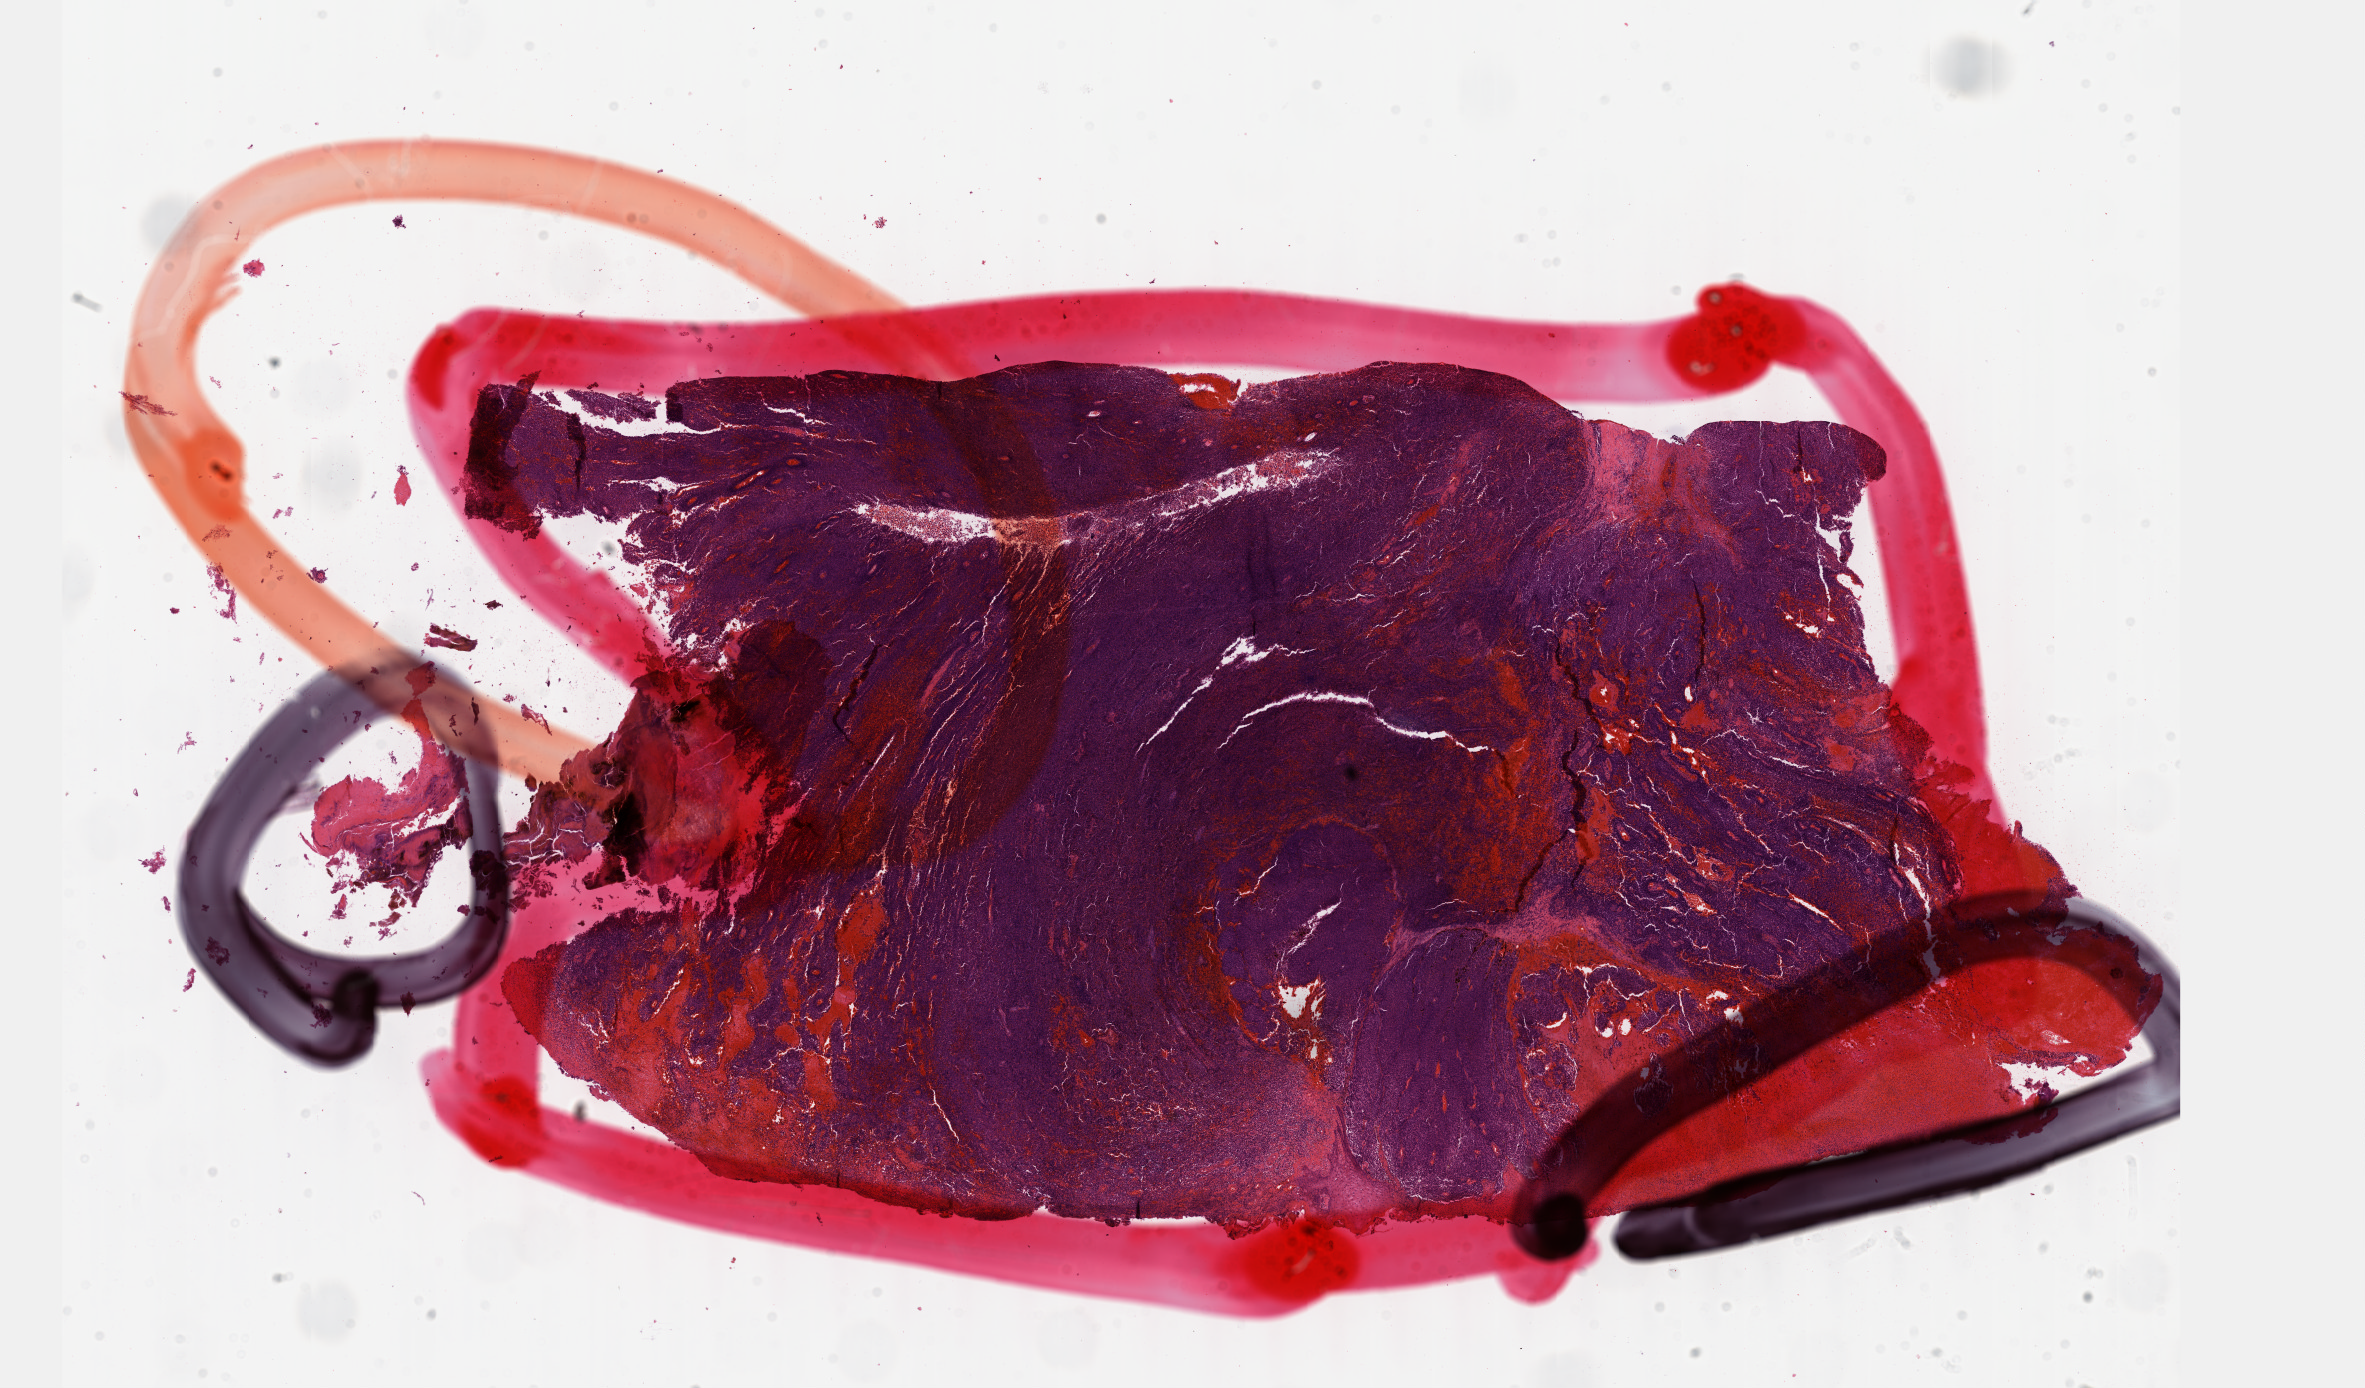
H&E whole-slide image — a low-resolution overview of the entire scanned area, about 19.1 x 11.2 mm; formalin-fixed paraffin-embedded (FFPE) diagnostic section; primary tumour sample from the skin. Female patient; age at initial diagnosis 66 years.
AJCC pathologic stage: IIB. Pathologic diagnosis: Malignant melanoma, NOS. TNM: T4a N0 M0.